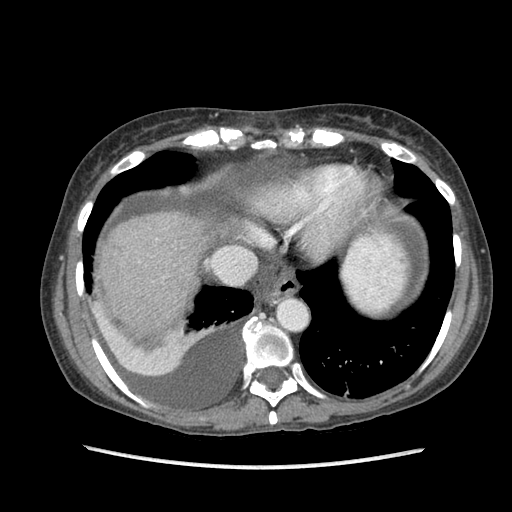
Contrast-enhanced abdominal CT (liver protocol), one axial slice. Slice 78 of 87 in the series (ordered by position). Soft-tissue window (W 400 / L 40 HU). 2.5 mm slice thickness. 512 × 512 image matrix, field of view 340 × 340 mm. From the clinical record (not read from this slice): diagnosis: hepatocellular carcinoma (patient treated with transarterial chemoembolisation; whether this scan precedes or follows treatment is not stated here); TNM stage (as recorded): Stage-IIIB; Child-Pugh class: A; tumour differentiation: no biopsy; tumour nodularity: uninodular.
Annotated regions visible in this slice (semi-automatically segmented with operator editing):
- liver parenchyma outside the tumour (the mass and vessels are separate outlines, so this box may not span the whole liver): bounding box (x1, y1, x2, y2) in pixels: (100, 212, 229, 314)